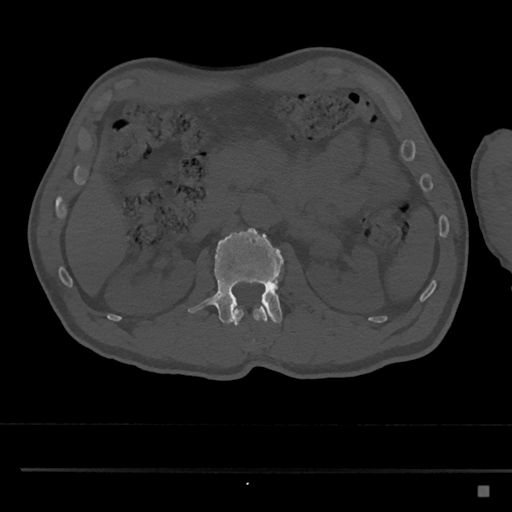
CT including the spine, one axial slice; bone window (W 1800 / L 400 HU); 0.5 mm slice thickness; 512 × 512 image matrix, field of view 391 × 391 mm. Patient: male, 59 years. Case-level facts recorded for this patient, not image findings: primary cancer: prostate.
Structures marked on this image (semi-automatically segmented with operator editing):
- L1 vertebra: bounding box (x1, y1, x2, y2) in pixels: (233, 306, 269, 325)
- L2 vertebra: (188, 228, 284, 325)